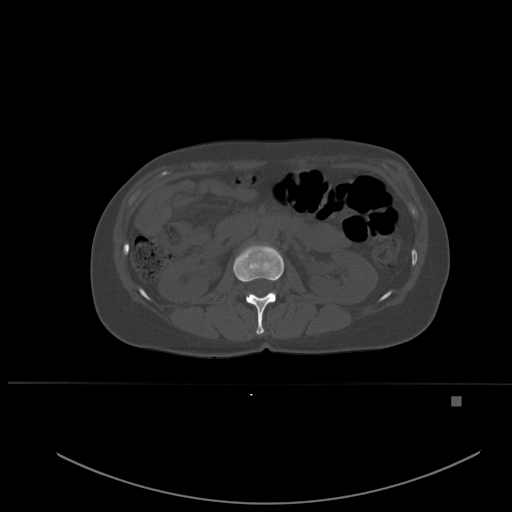
CT including the spine, one axial slice. Slice 229 of 651 in the series (ordered by position). Bone window (W 1800 / L 400 HU). 512 × 512 image matrix. Female patient, age 49 years. From the clinical record (not read from this slice): primary cancer: breast; vertebrae with lytic lesions (as recorded): L3, T12, L4.
Outlined on this slice (semi-automatic segmentation, software-assisted and operator-edited):
- L1 vertebra: bounding box (x1, y1, x2, y2) in pixels: (233, 243, 284, 334)